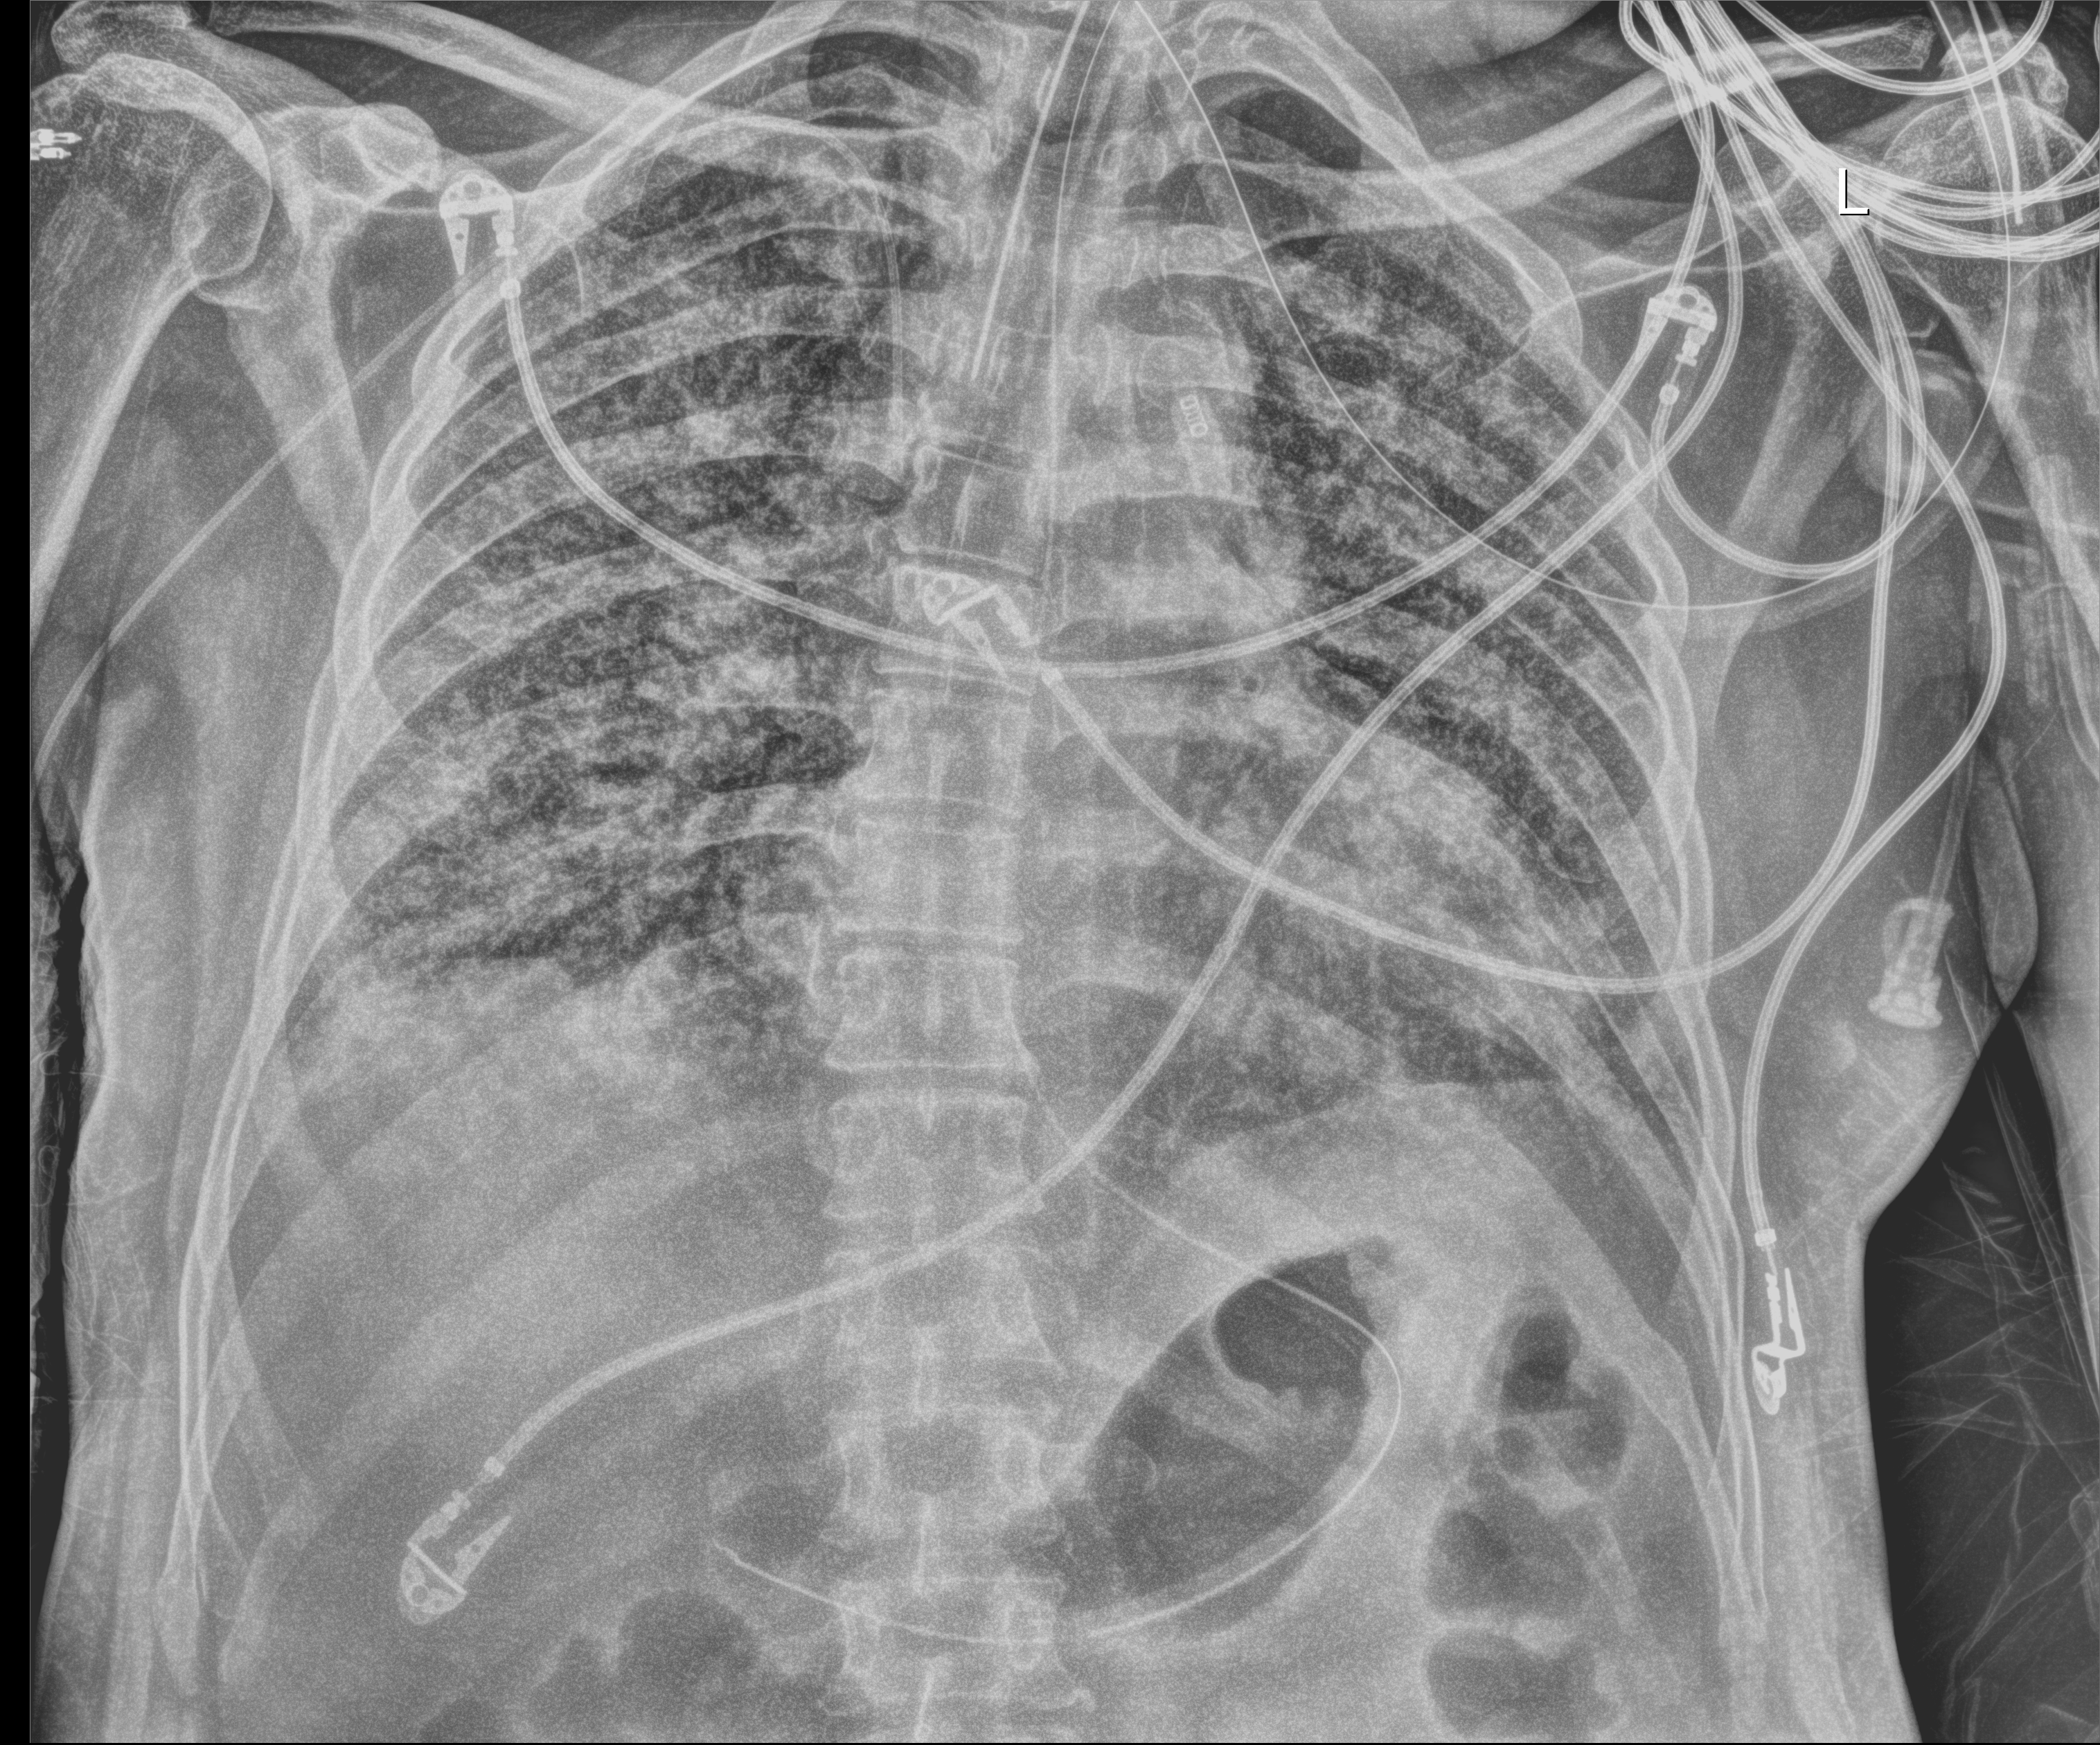
Portable chest radiograph; anteroposterior (AP) projection. Male patient hospitalised with COVID-19, age 60–74 years.
Hospital-stay facts (about this admission, not read from this image; timing relative to this image not recorded): mechanically ventilated during this hospital stay: yes; diabetes (admission record): no; admitted to intensive care during this hospital stay: yes.